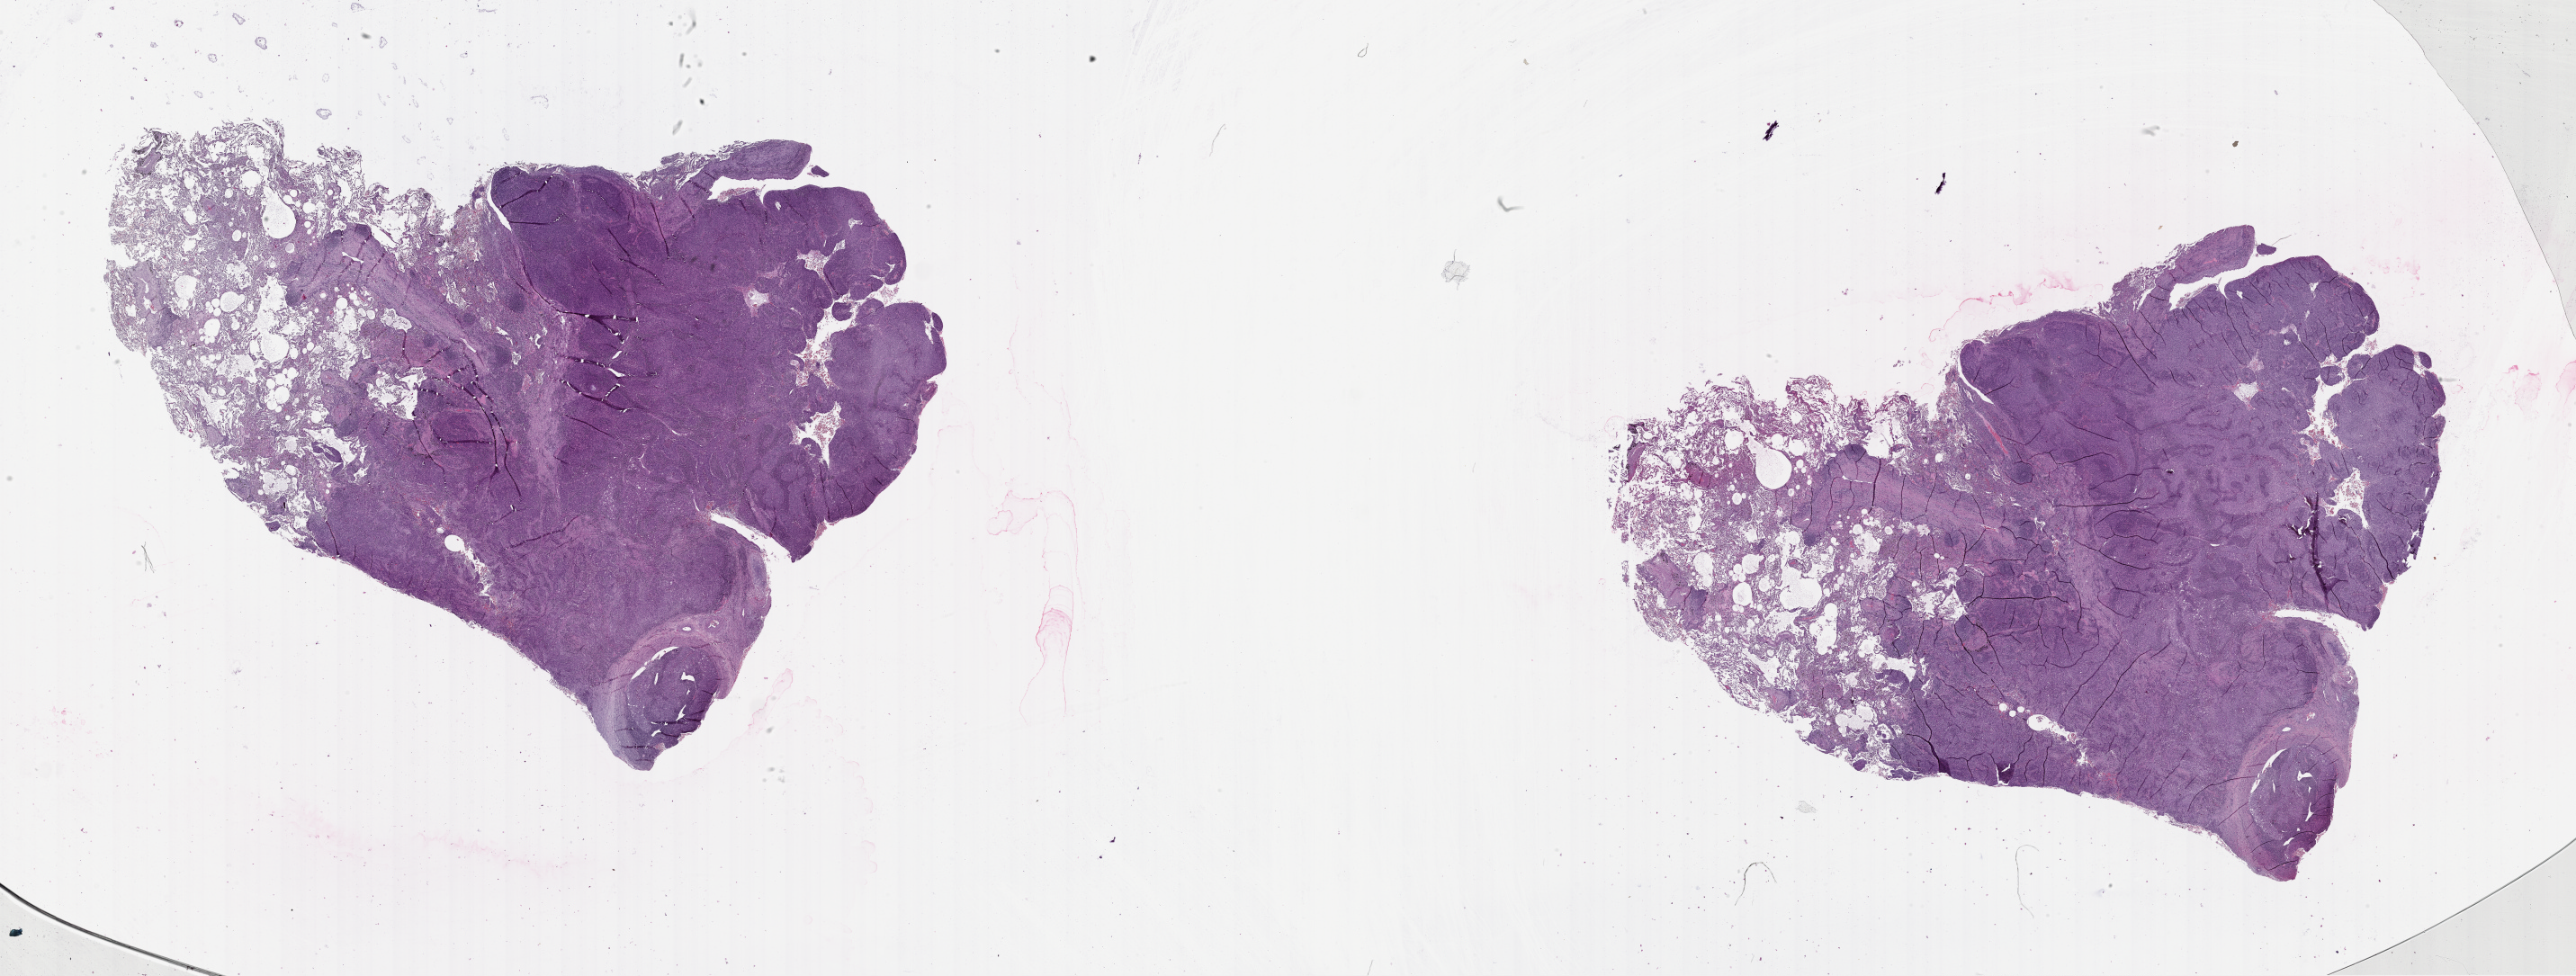
Digitized H&E-stained tissue section (whole slide) — a low-resolution overview of the entire scanned area, about 46.1 x 17.5 mm. Lung, tumour tissue. 65-year-old male patient.
Patient diagnosis (cohort enrolment): squamous cell carcinoma (lung).